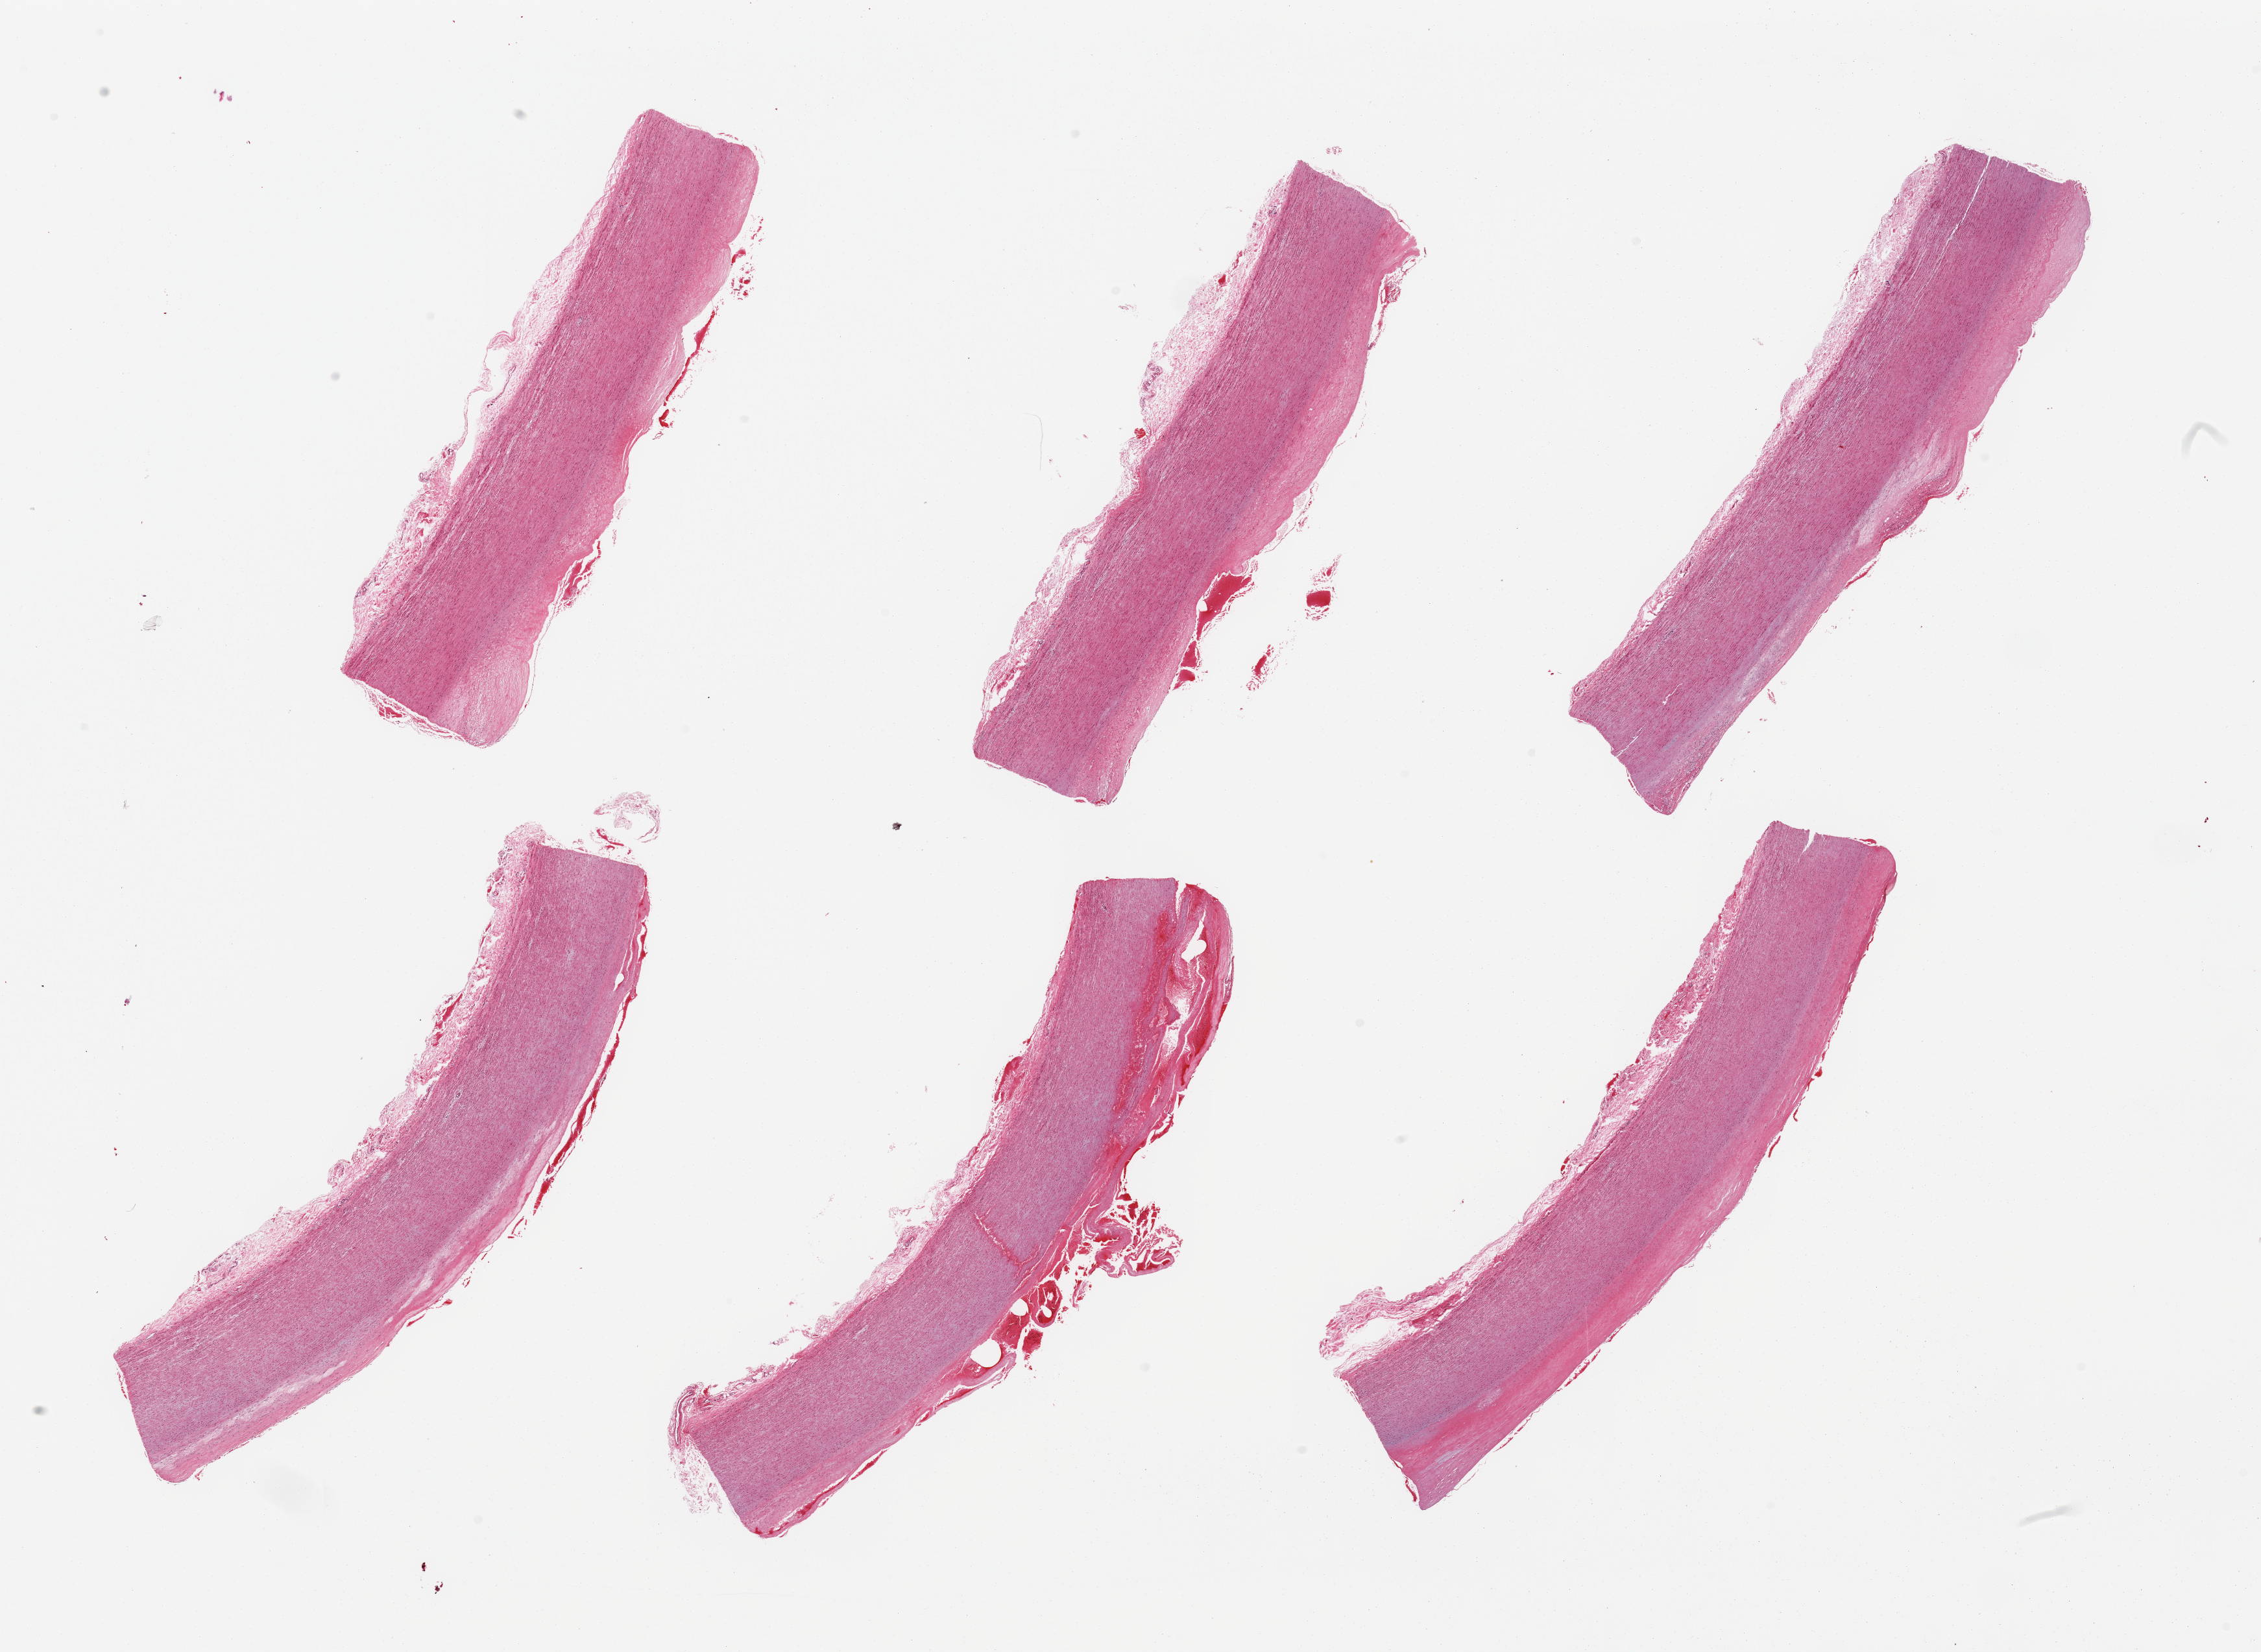
Haematoxylin and eosin whole-slide image, brightfield — whole scanned area (about 27.6 x 20.1 mm) shown as a low-resolution overview. PAXgene-fixed paraffin-embedded (PFPE) section. Sampled site (target tissue): aorta. Tissue donor sample. Donor: male.
Reviewer comment on this tissue sample: 6 pieces; mild to moderate autolysis; marked atherosclerosis with slerotic, ulcerated plaque and superficial dissection and fresh thrombosis; up to 0.7mm attached adventitia.